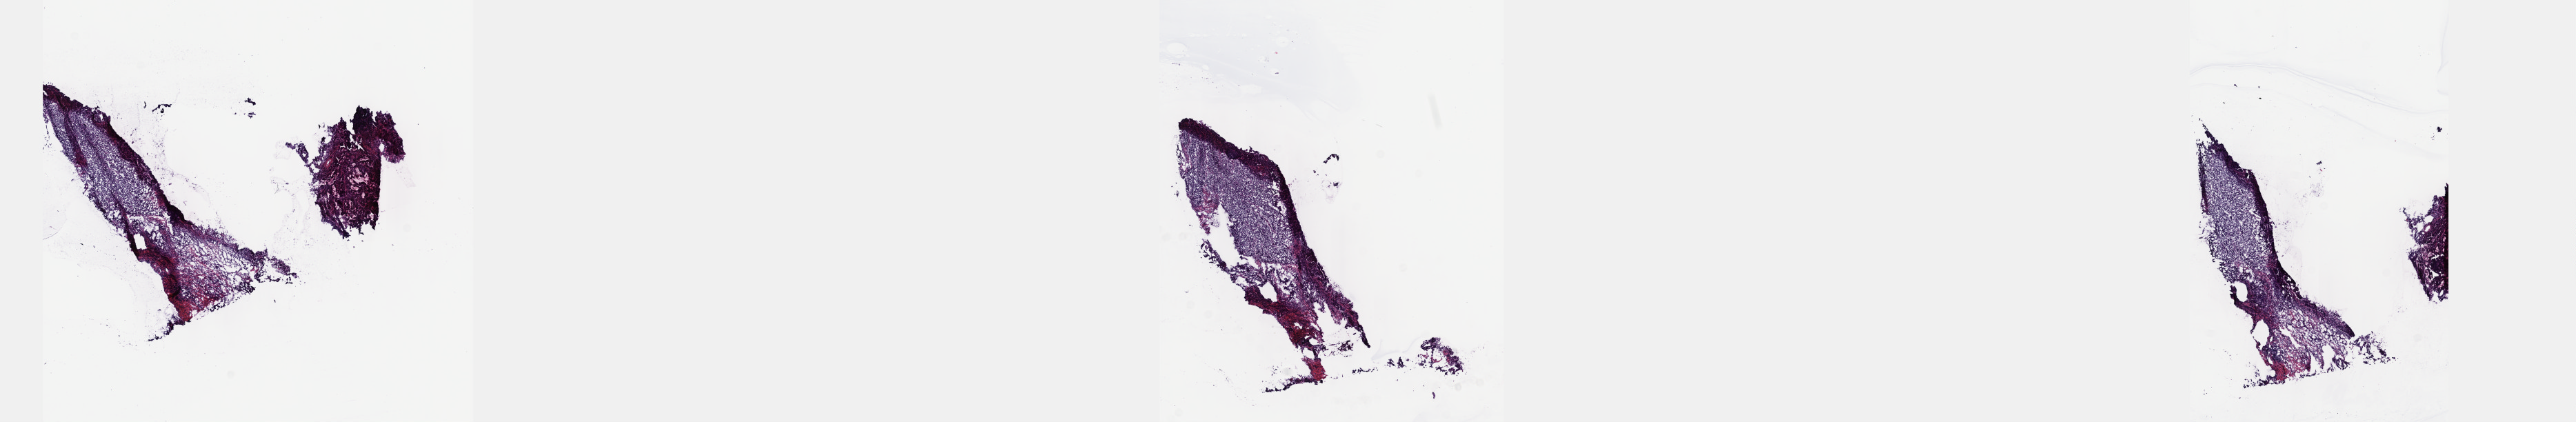
Digitized H&E-stained tissue section (whole slide) — low-resolution overview of the scanned area, about 30.2 x 4.9 mm (from a 40x scan); frozen section from the top of the tissue portion; primary tumour sample from the stomach. Male, age 79 years at initial diagnosis. Histologic grade: G3 (poorly differentiated). Pathologist review of this section (percent, as recorded): tumour cells 100%, tumour nuclei 80%, normal cells 0%, stromal cells 0%, necrosis 0%. Infiltration values recorded for this section: lymphocyte infiltration 4%, monocyte infiltration 0%, neutrophil infiltration 0%.
AJCC pathologic stage: IIA (7th edition). Diagnosis: Adenocarcinoma, NOS (gastric antrum). TNM: T3 N0 M0.